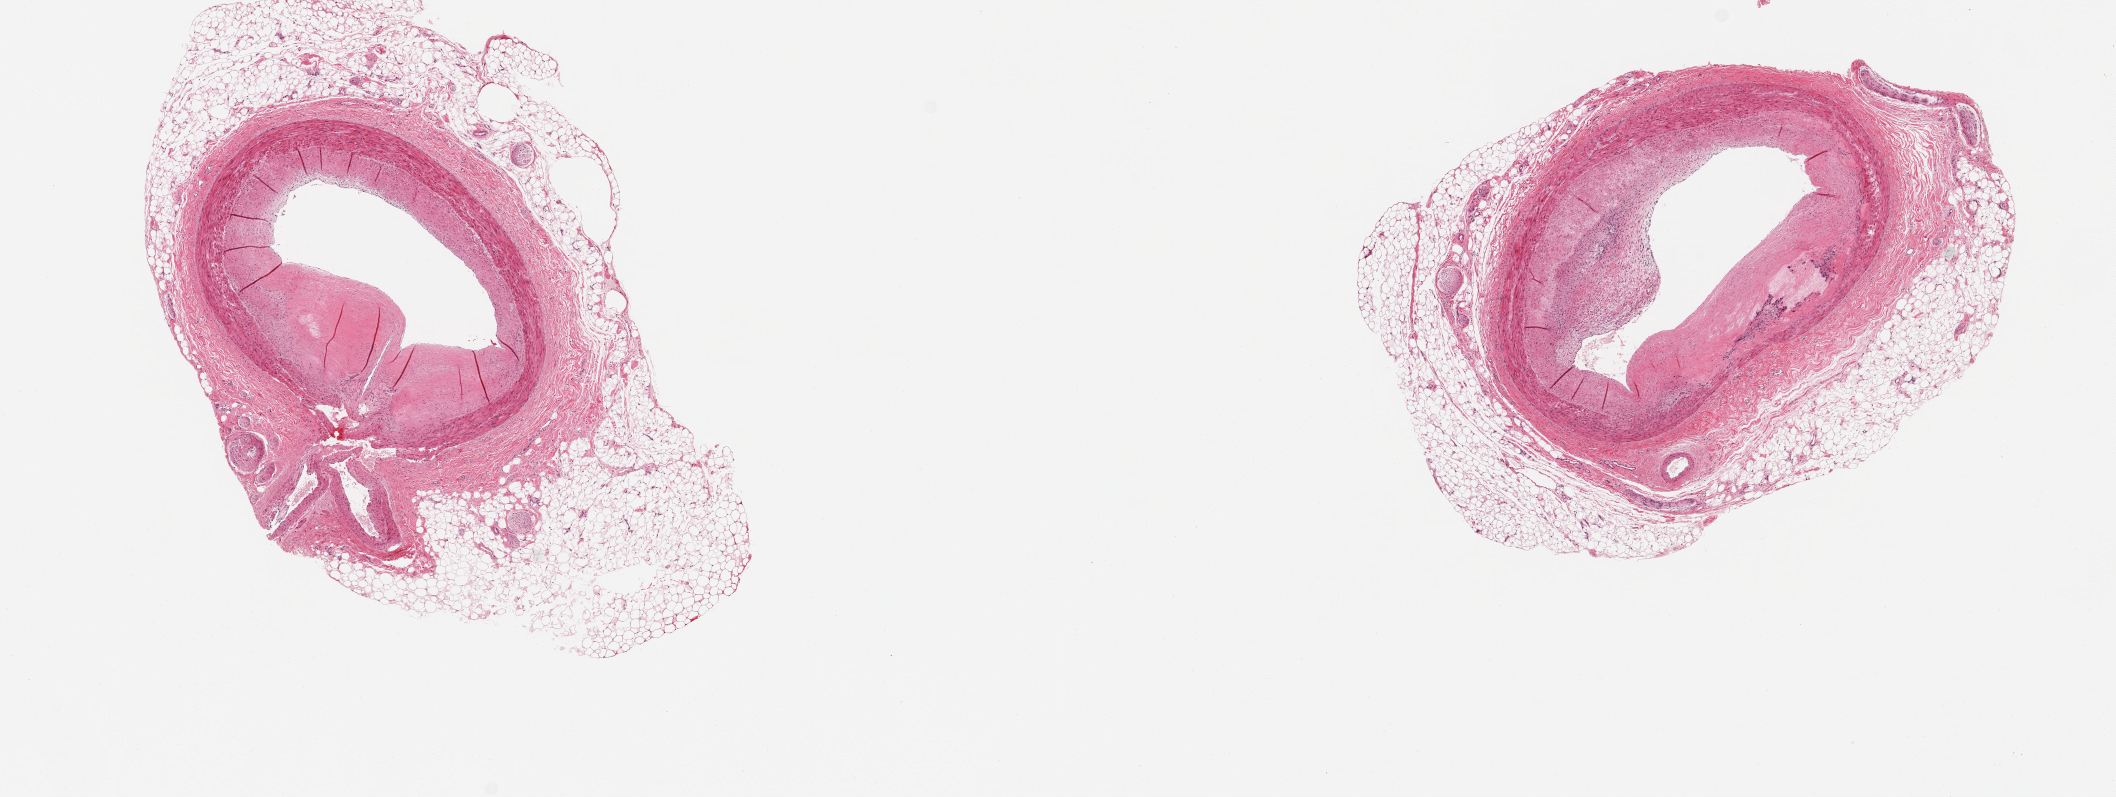
Haematoxylin and eosin whole-slide image, whole scanned area (about 16.7 x 6.3 mm) shown as a low-resolution overview, PAXgene-fixed paraffin-embedded (PFPE) section, sampled site (target tissue): coronary artery, tissue donor sample. Donor: male.
• review note (as recorded): 2 pieces, ~50-60% occlusive atherosis, both sections with rims of adherent fat, up to ~0.8 mm